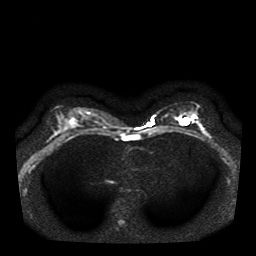
Breast MRI, one axial slice. Slice 21 of 41 in the series (ordered by position). Diffusion-weighted series; image 2 of 4 stored at this slice position (different b-values; order by instance number). 1.5 T. 256 × 256 image matrix, field of view 330 × 330 mm. Female patient.
Outlined on this slice (expert manual segmentation):
- tumour on diffusion-weighted imaging: box from (x=192, y=115) to (x=197, y=122) px